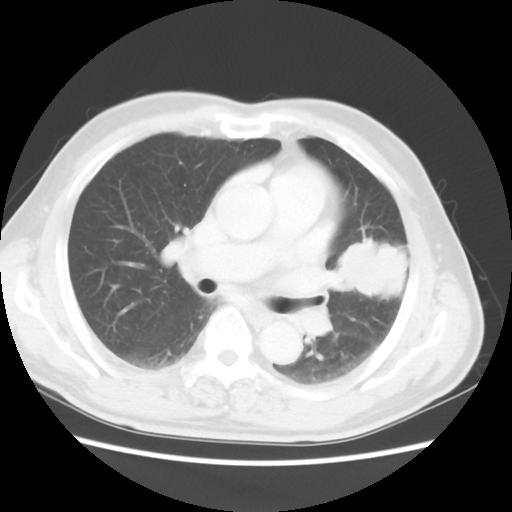
Chest CT, one axial slice; slice 28 of 50 in the series (ordered by position); reconstruction kernel STANDARD; 120 kVp; lung window (W 1500 / L -600 HU); 5 mm slice thickness; 512 × 512 image matrix, field of view 360 × 360 mm. Patient: male, 69 years. Case-level facts recorded for this patient, not image findings: clinical TNM (as recorded): T3 N1 M1a.
Annotated regions visible in this slice (bounding box drawn by a radiologist):
- lung tumour (recorded histology: squamous cell carcinoma): bounding box (x1, y1, x2, y2) in pixels: (342, 236, 416, 309)